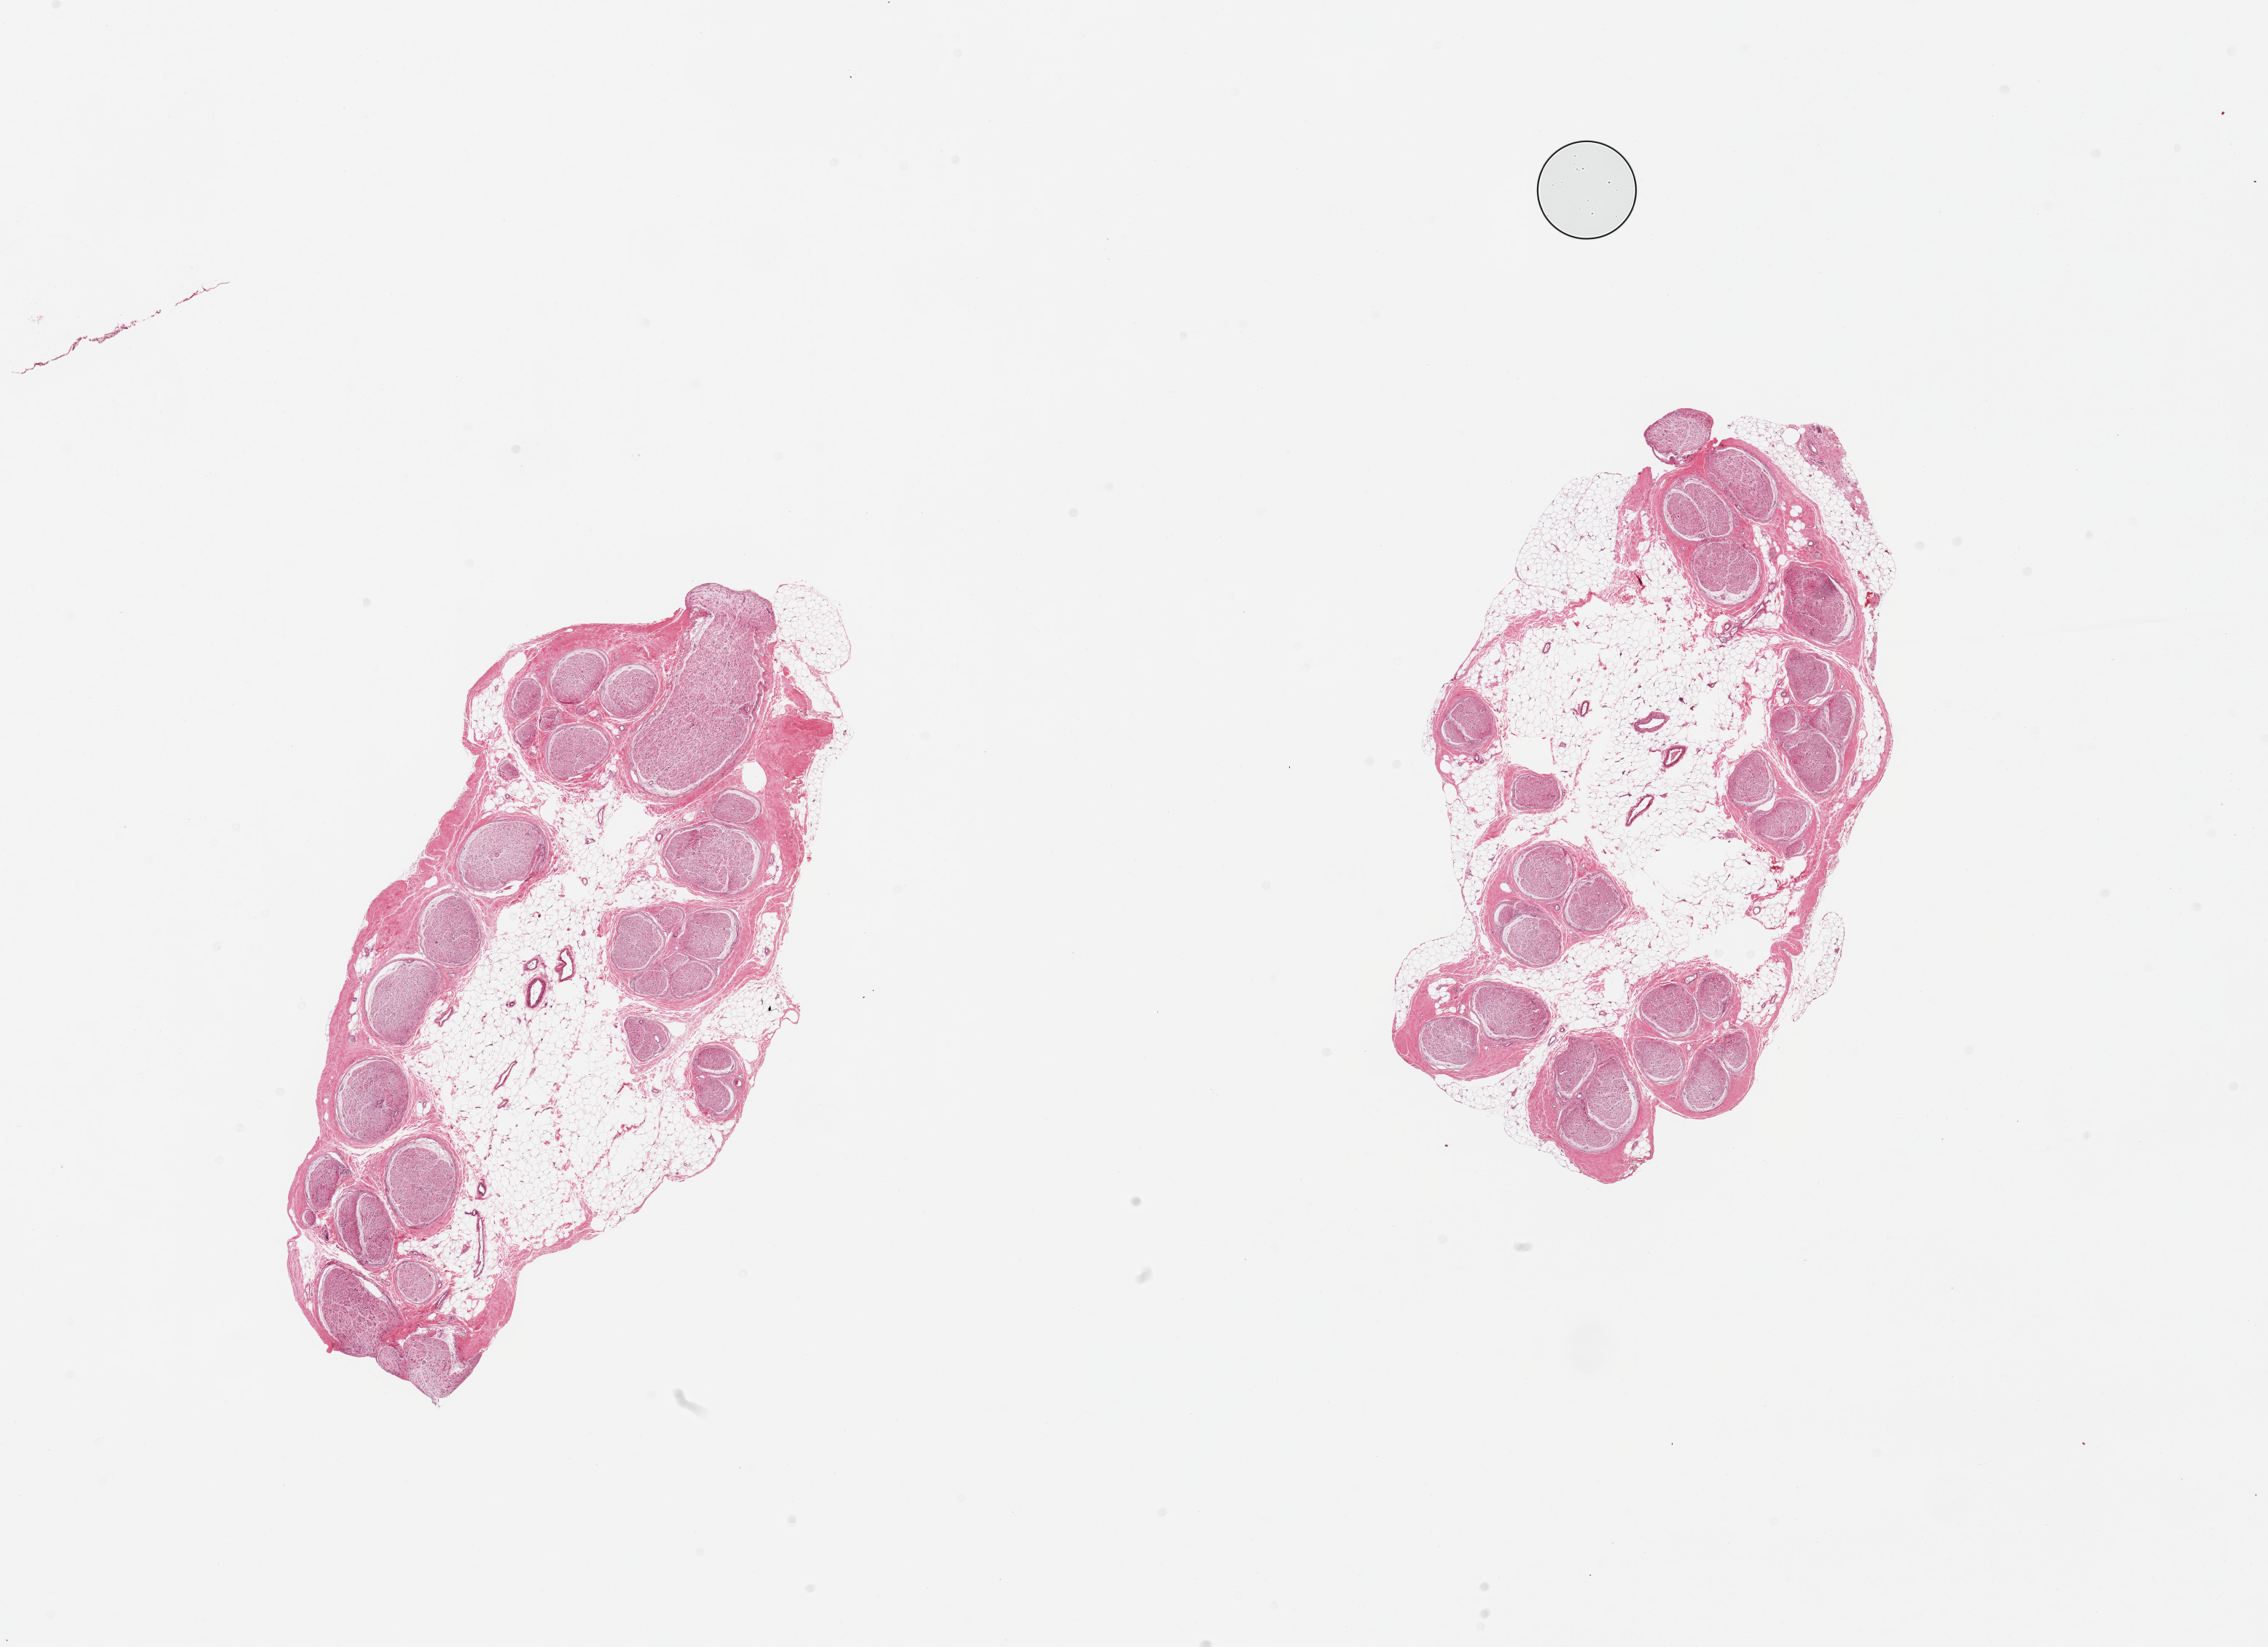
Digitized hematoxylin and eosin (H&E)-stained section, a low-resolution overview of the entire scanned area, about 24.6 x 17.9 mm; PAXgene-fixed, paraffin-embedded tissue; target tissue: tibial nerve; donor tissue sample. Male donor.
Pathologist's review note for this sample: 2 pieces, relatively clean sections.